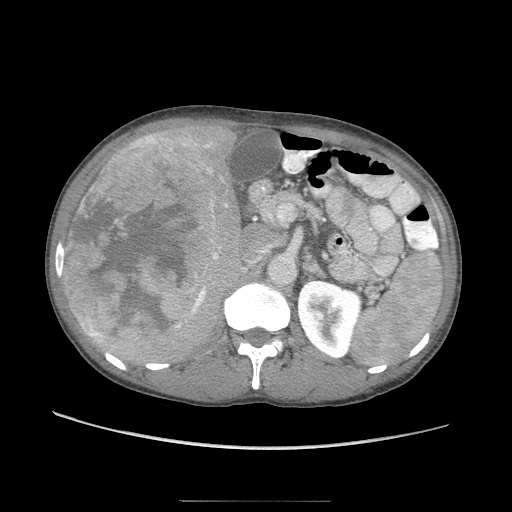
Contrast-enhanced abdominal CT (liver protocol), one axial slice; slice 43 of 103 in the series (ordered by position); reconstruction kernel STANDARD; 120 kVp; soft-tissue window (W 400 / L 40 HU); 2.5 mm slice thickness; 512 × 512 image matrix, field of view 380 × 380 mm. From the clinical record (not read from this slice): diagnosis: hepatocellular carcinoma (patient treated with transarterial chemoembolisation; whether this scan precedes or follows treatment is not stated here); TNM stage (as recorded): Stage-IIIA; Child-Pugh class: A; tumour differentiation: moderately differentiated; tumour nodularity: multinodular.
Annotated regions visible in this slice (semi-automatic segmentation, software-assisted and operator-edited):
- liver parenchyma outside the tumour (the mass and vessels are separate outlines, so this box may not span the whole liver): bounding box [x1, y1, x2, y2] px = [62, 122, 251, 363]
- mass: [63, 131, 220, 347]
- liver vessels: [202, 146, 222, 253]